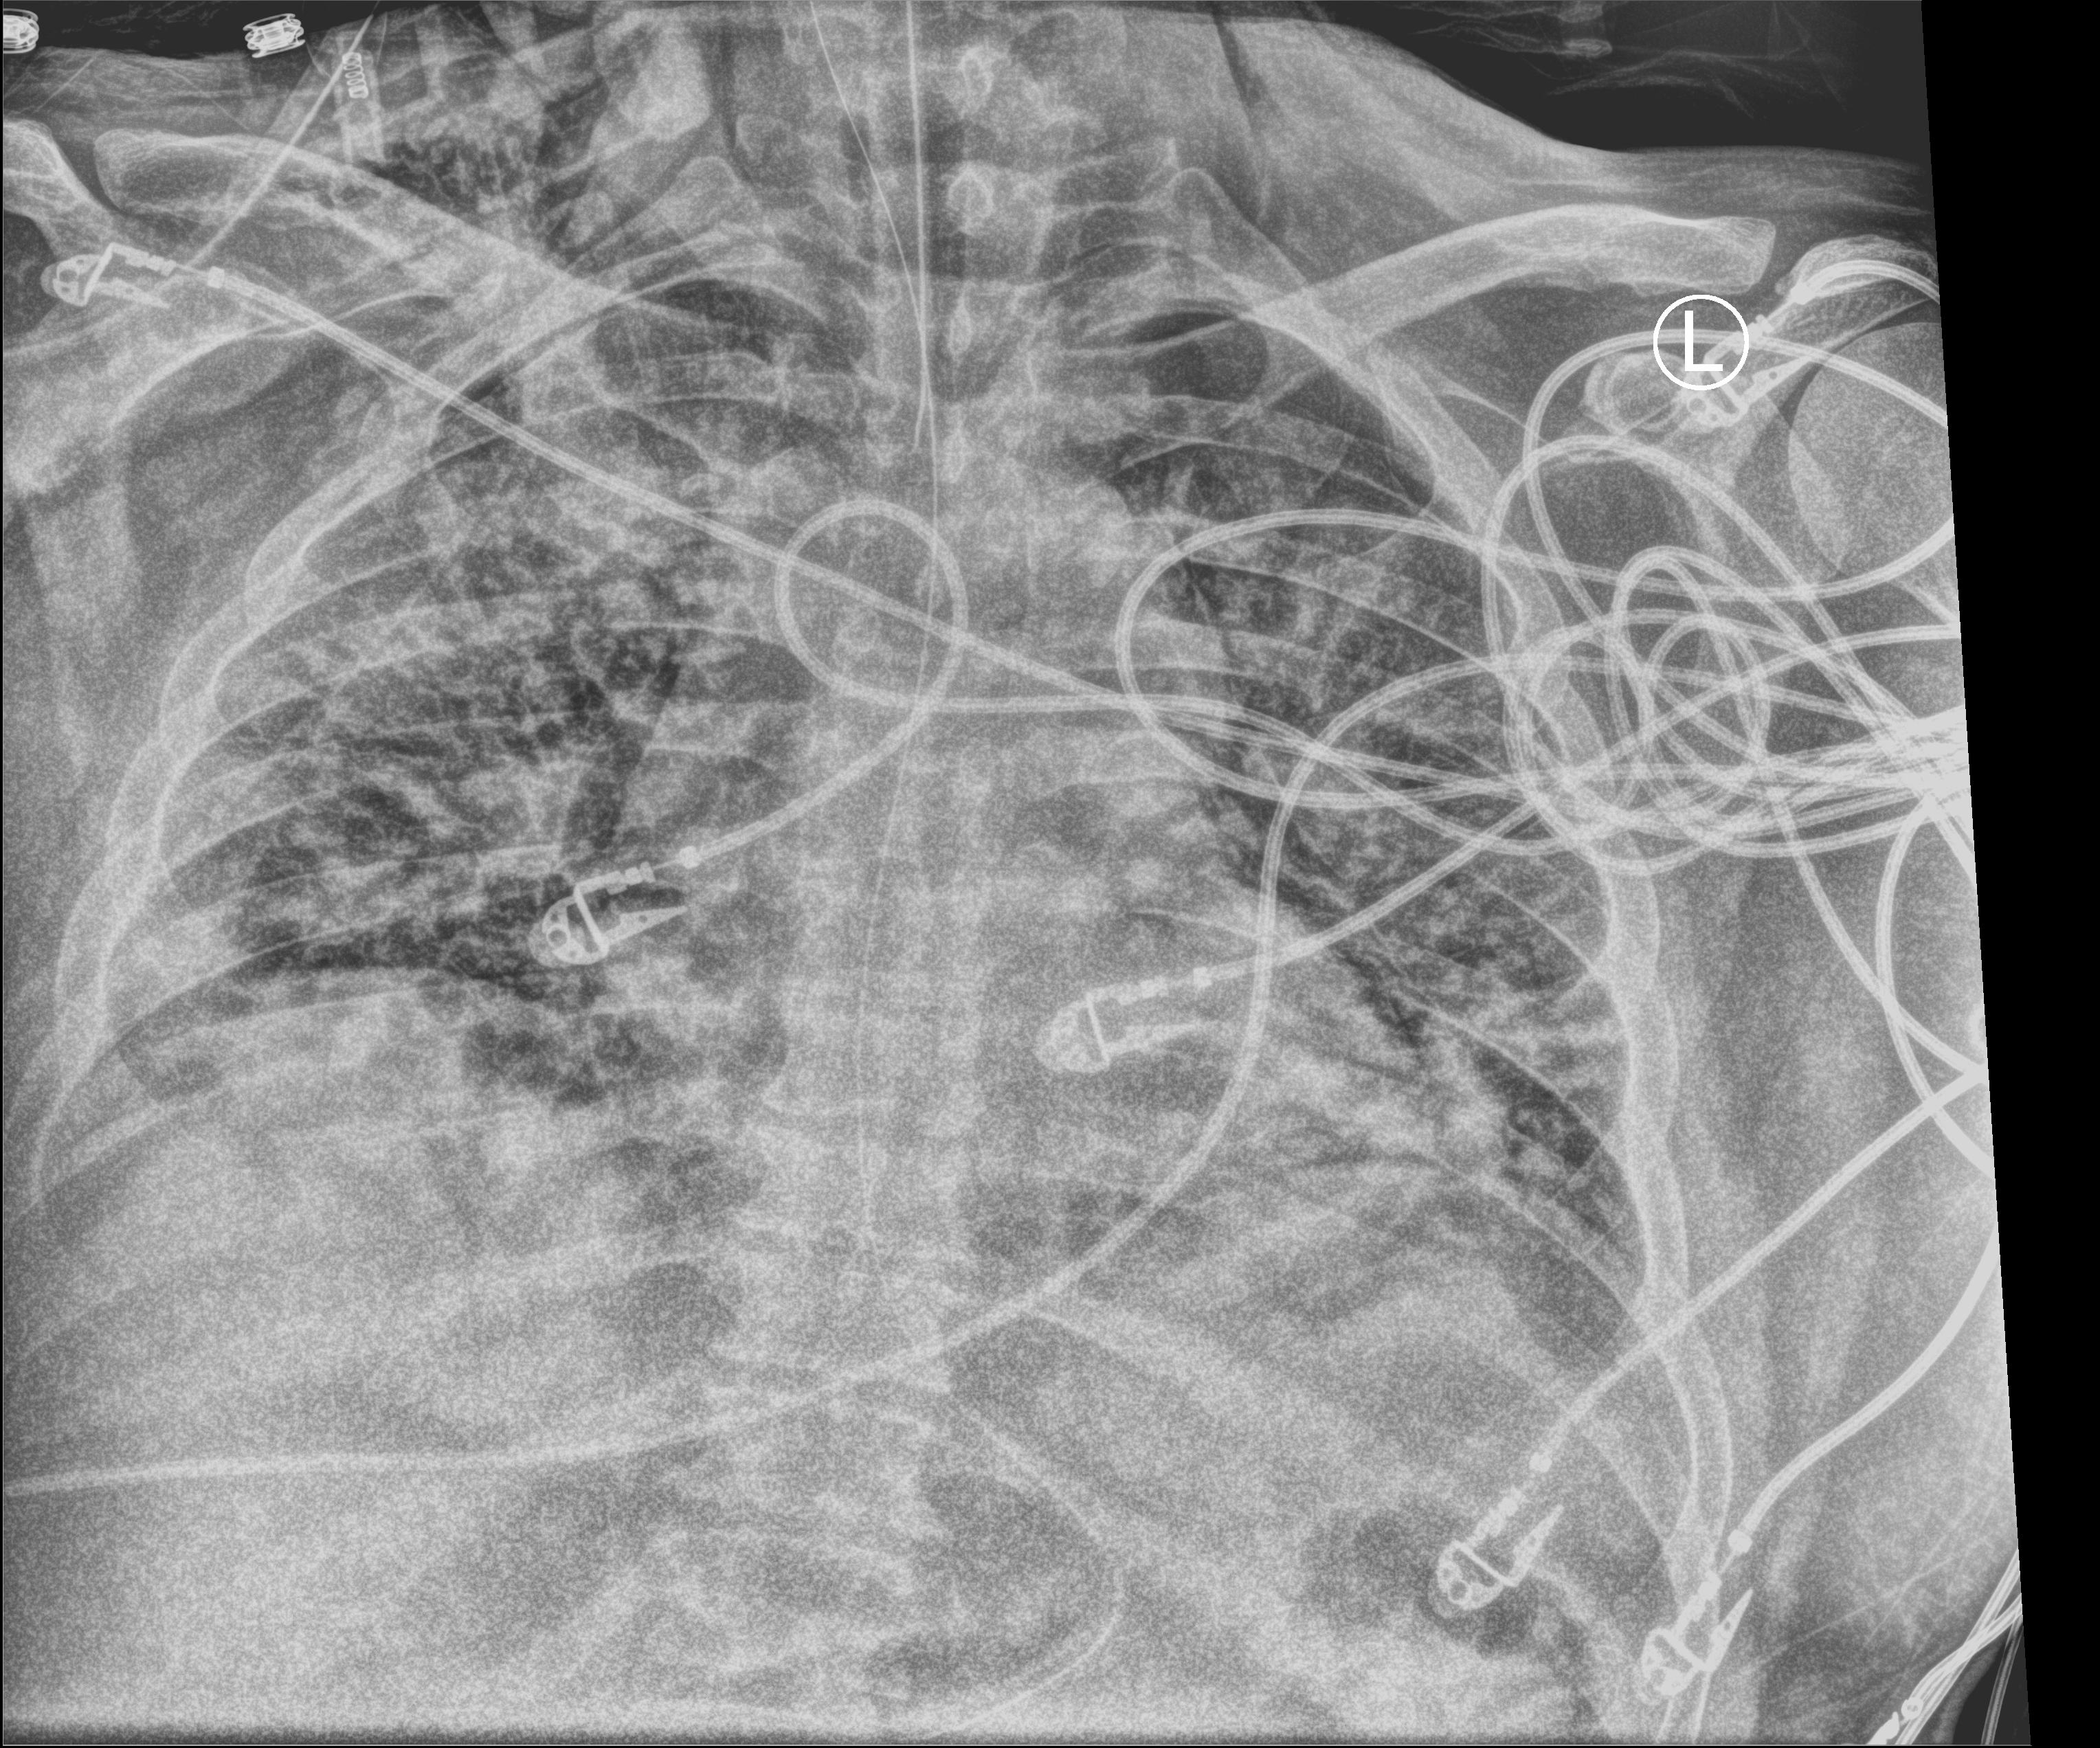
Bedside chest radiograph (computed radiography), anteroposterior (AP) projection. Patient hospitalised with COVID-19, aged 18–59 years.
Admission-level facts for this patient (not findings on this image; timing relative to this image not recorded):
- length of hospital stay: 31 days